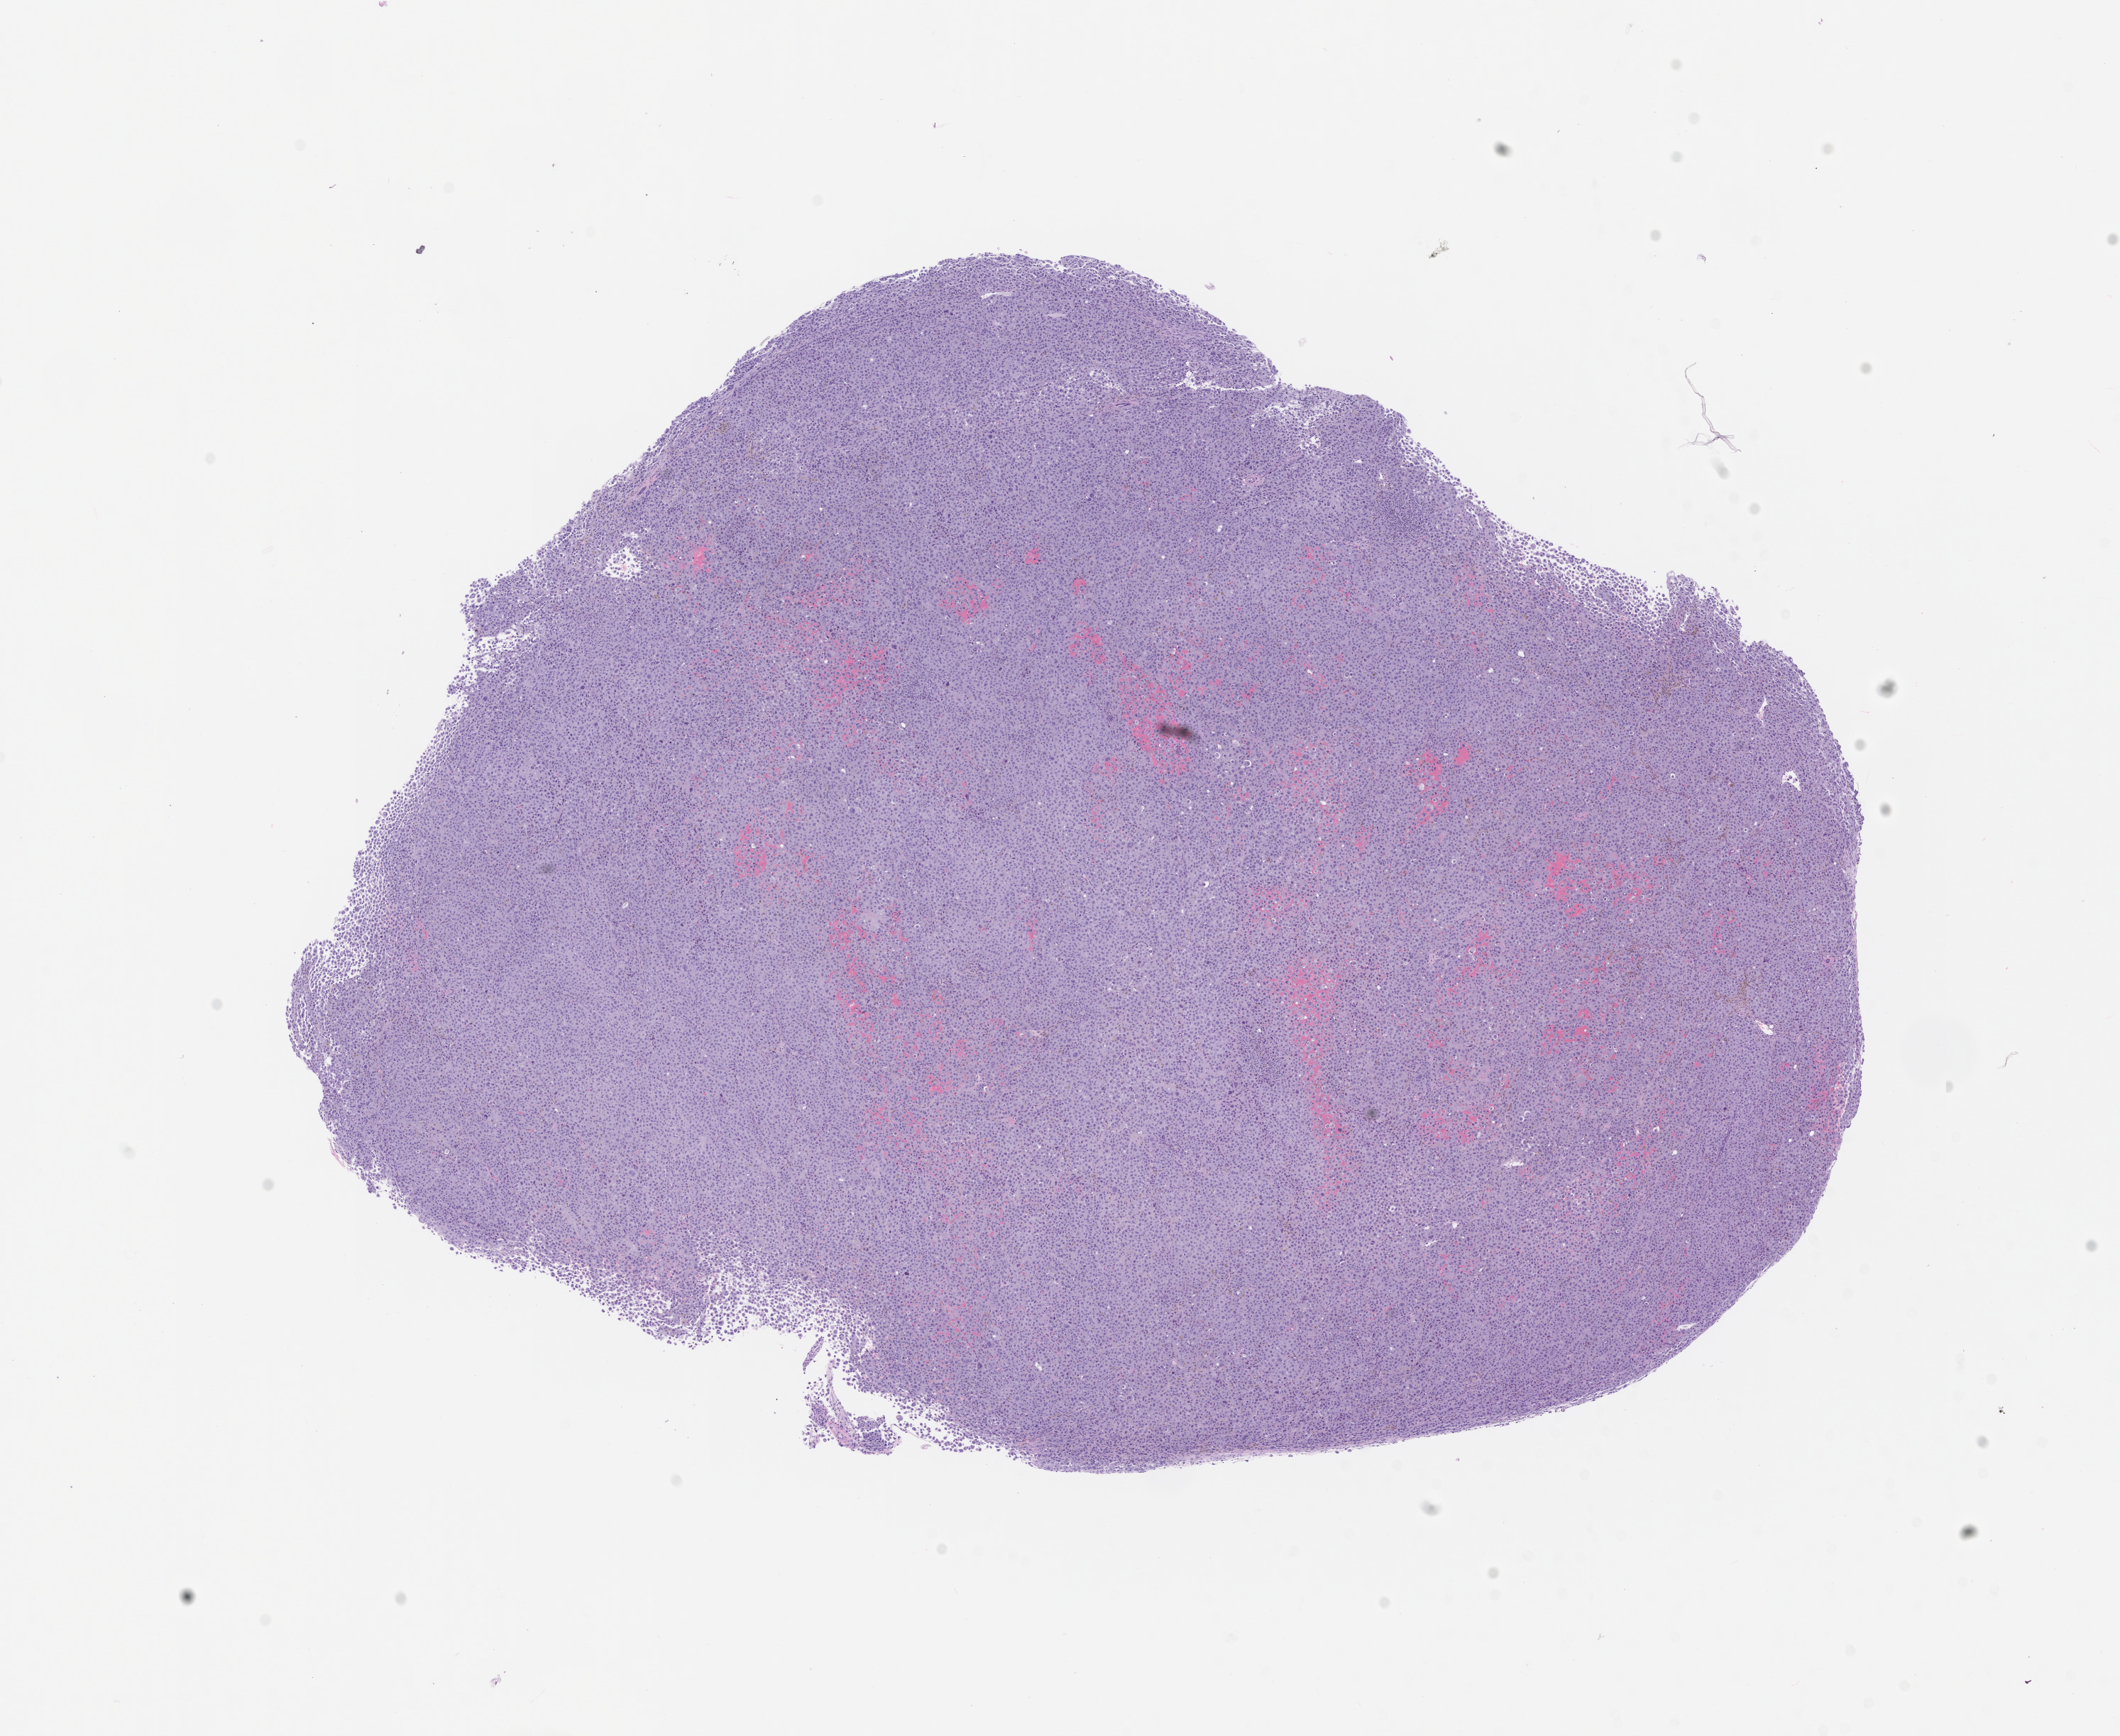
Whole-slide image, H&E: patient-derived xenograft (human tumor grown in a mouse), passage 1 — shown as a low-resolution overview of the whole scanned area (about 12.0 x 9.8 mm), FFPE section, tumor site category: skin.
• originating patient diagnosis: Melanoma